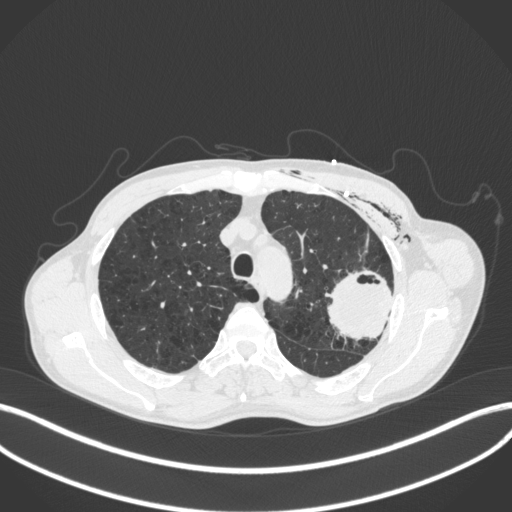
Chest CT, one axial slice; 120 kVp; lung window (W 1500 / L -600 HU); 1 mm slice thickness; 512 × 512 image matrix. Patient: male, 58 years. From the clinical record (not read from this slice): clinical TNM (as recorded): T3 N0 M0.
Outlined on this slice (bounding box drawn by a radiologist):
- lung tumour (recorded histology: adenocarcinoma): box from (x=320, y=266) to (x=398, y=340) px